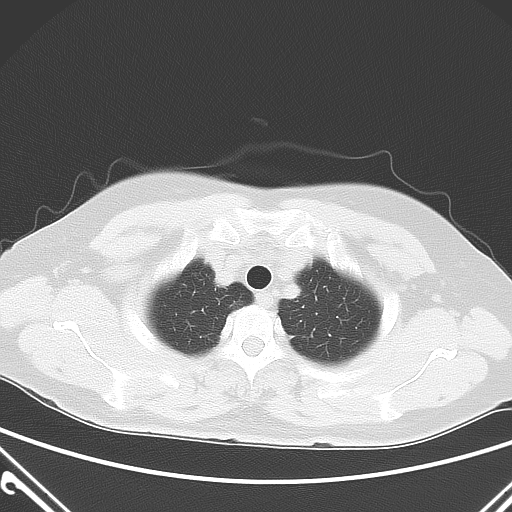
Chest CT, one axial slice; position 50 of 60 along the scan axis; 120 kVp; lung window (W 1500 / L -600 HU); 512 × 512 image matrix, field of view 350 × 350 mm. Female patient, age 54 years. Case-level facts recorded for this patient, not image findings: clinical TNM (as recorded): T1a N0 M0; histopathological grade: G1.
Annotated regions visible in this slice (rectangle marked by the reading radiologist):
- lung tumour (recorded histology: adenocarcinoma): bounding box <227,296,250,315> (left, top, right, bottom; pixels)